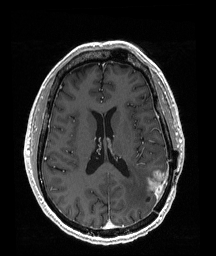
Brain MRI from a brain-tumour surgery series, one axial slice. Slice 81 of 192 in the series (ordered by position). T1-weighted post-contrast. 1 mm slice thickness. 216 × 256 image matrix, field of view 211 × 250 mm. From the clinical record (not read from this slice): histopathology: Glioblastoma; WHO grade: 4; IDH mutation: no; tumour location: Left Temporoparietal.
Outlined on this slice (expert manual segmentation):
- tumour: bounding box <144,172,170,197> (left, top, right, bottom; pixels)